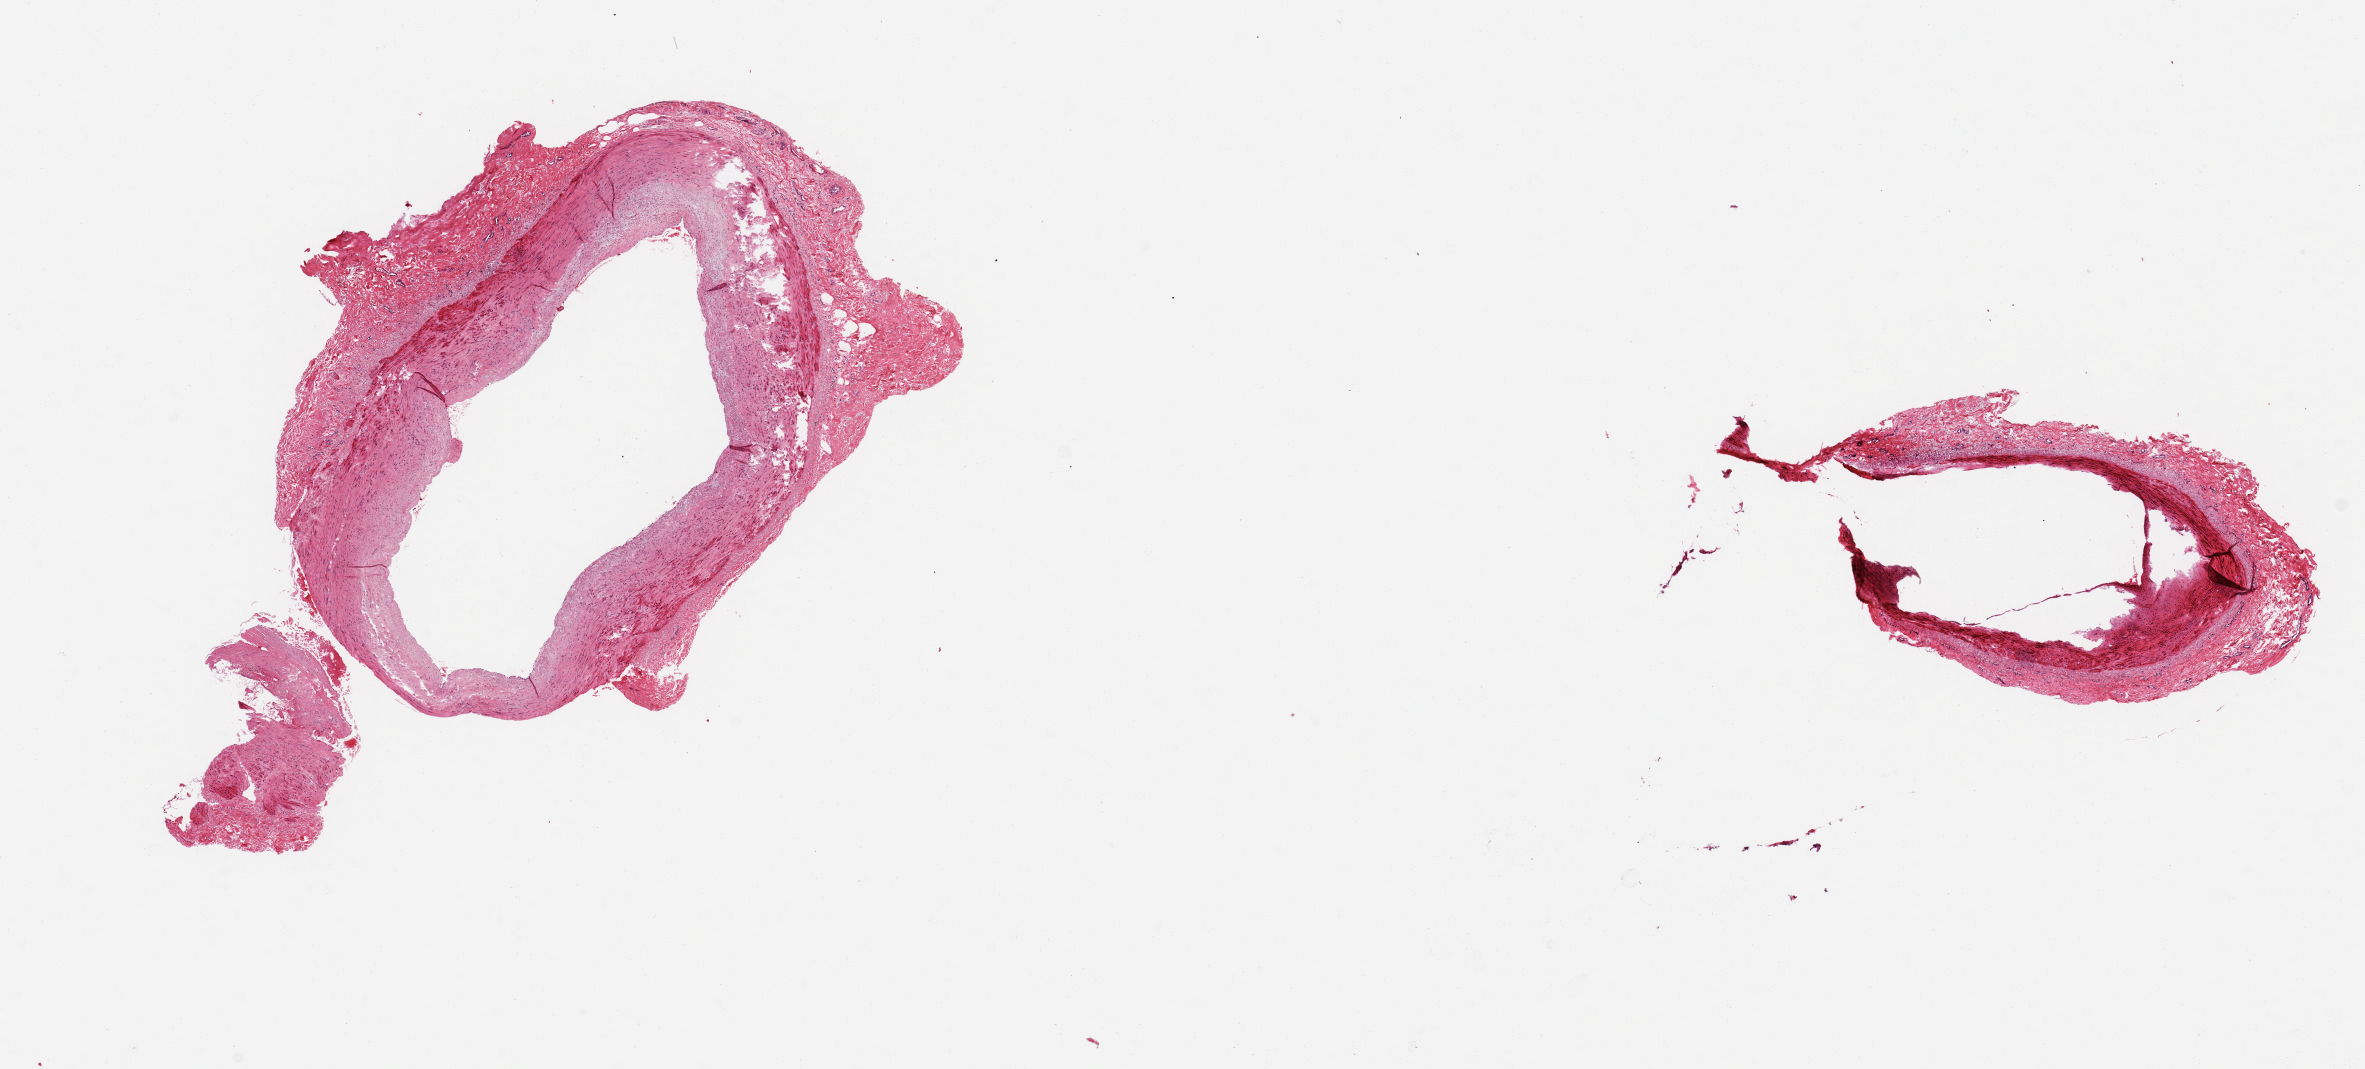
Whole-slide image, haematoxylin and eosin stain, brightfield, whole scanned area (about 18.7 x 8.5 mm, slide scanned at 20x) shown as a low-resolution overview, PAXgene-fixed, paraffin-embedded tissue, section of tibial artery (target tissue), donor tissue sample. Male donor.
Review note (as recorded): 2 pieces ~4mm d. Rim of fibrous tissue 0.5 --1mm around larger aliquot.